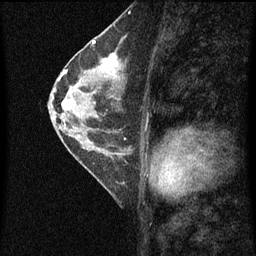
Breast MRI (dynamic contrast-enhanced), one sagittal slice; position 35 of 60 along the scan axis; dynamic contrast-enhanced series, image 2 of 4 at this slice position (ordered by acquisition); 1.5 T; TE 4.2 ms, TR 8 ms; 2 mm slice thickness; 256 × 256 image matrix. Patient: female, 56 years.
Outlined on this slice (semi-automatic segmentation, software-assisted and operator-edited):
- analysis volume of interest (the breast-tissue region the enhancement analysis was run in; not a lesion): box from (x=56, y=52) to (x=127, y=115) px
- tumour enhancement mask (voxels above the 70 % enhancement threshold inside the analysis volume of interest): (x=60, y=54)–(x=119, y=111)